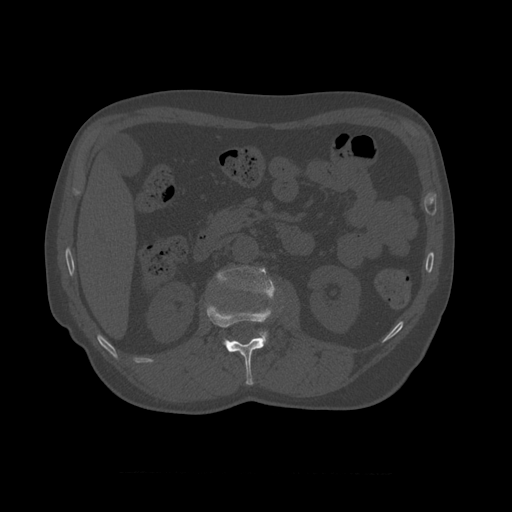
CT including the spine, one axial slice; slice 348 of 450 in the series (ordered by position); reconstruction kernel STANDARD; bone window (W 1800 / L 400 HU); 1.25 mm slice thickness; 512 × 512 image matrix. Patient age 75 years. Case-level facts recorded for this patient, not image findings: primary cancer: prostate.
Outlined on this slice (semi-automatic segmentation, software-assisted and operator-edited):
- L1 vertebra: bounding box [x1, y1, x2, y2] px = [206, 302, 273, 386]
- L2 vertebra: [213, 266, 277, 346]